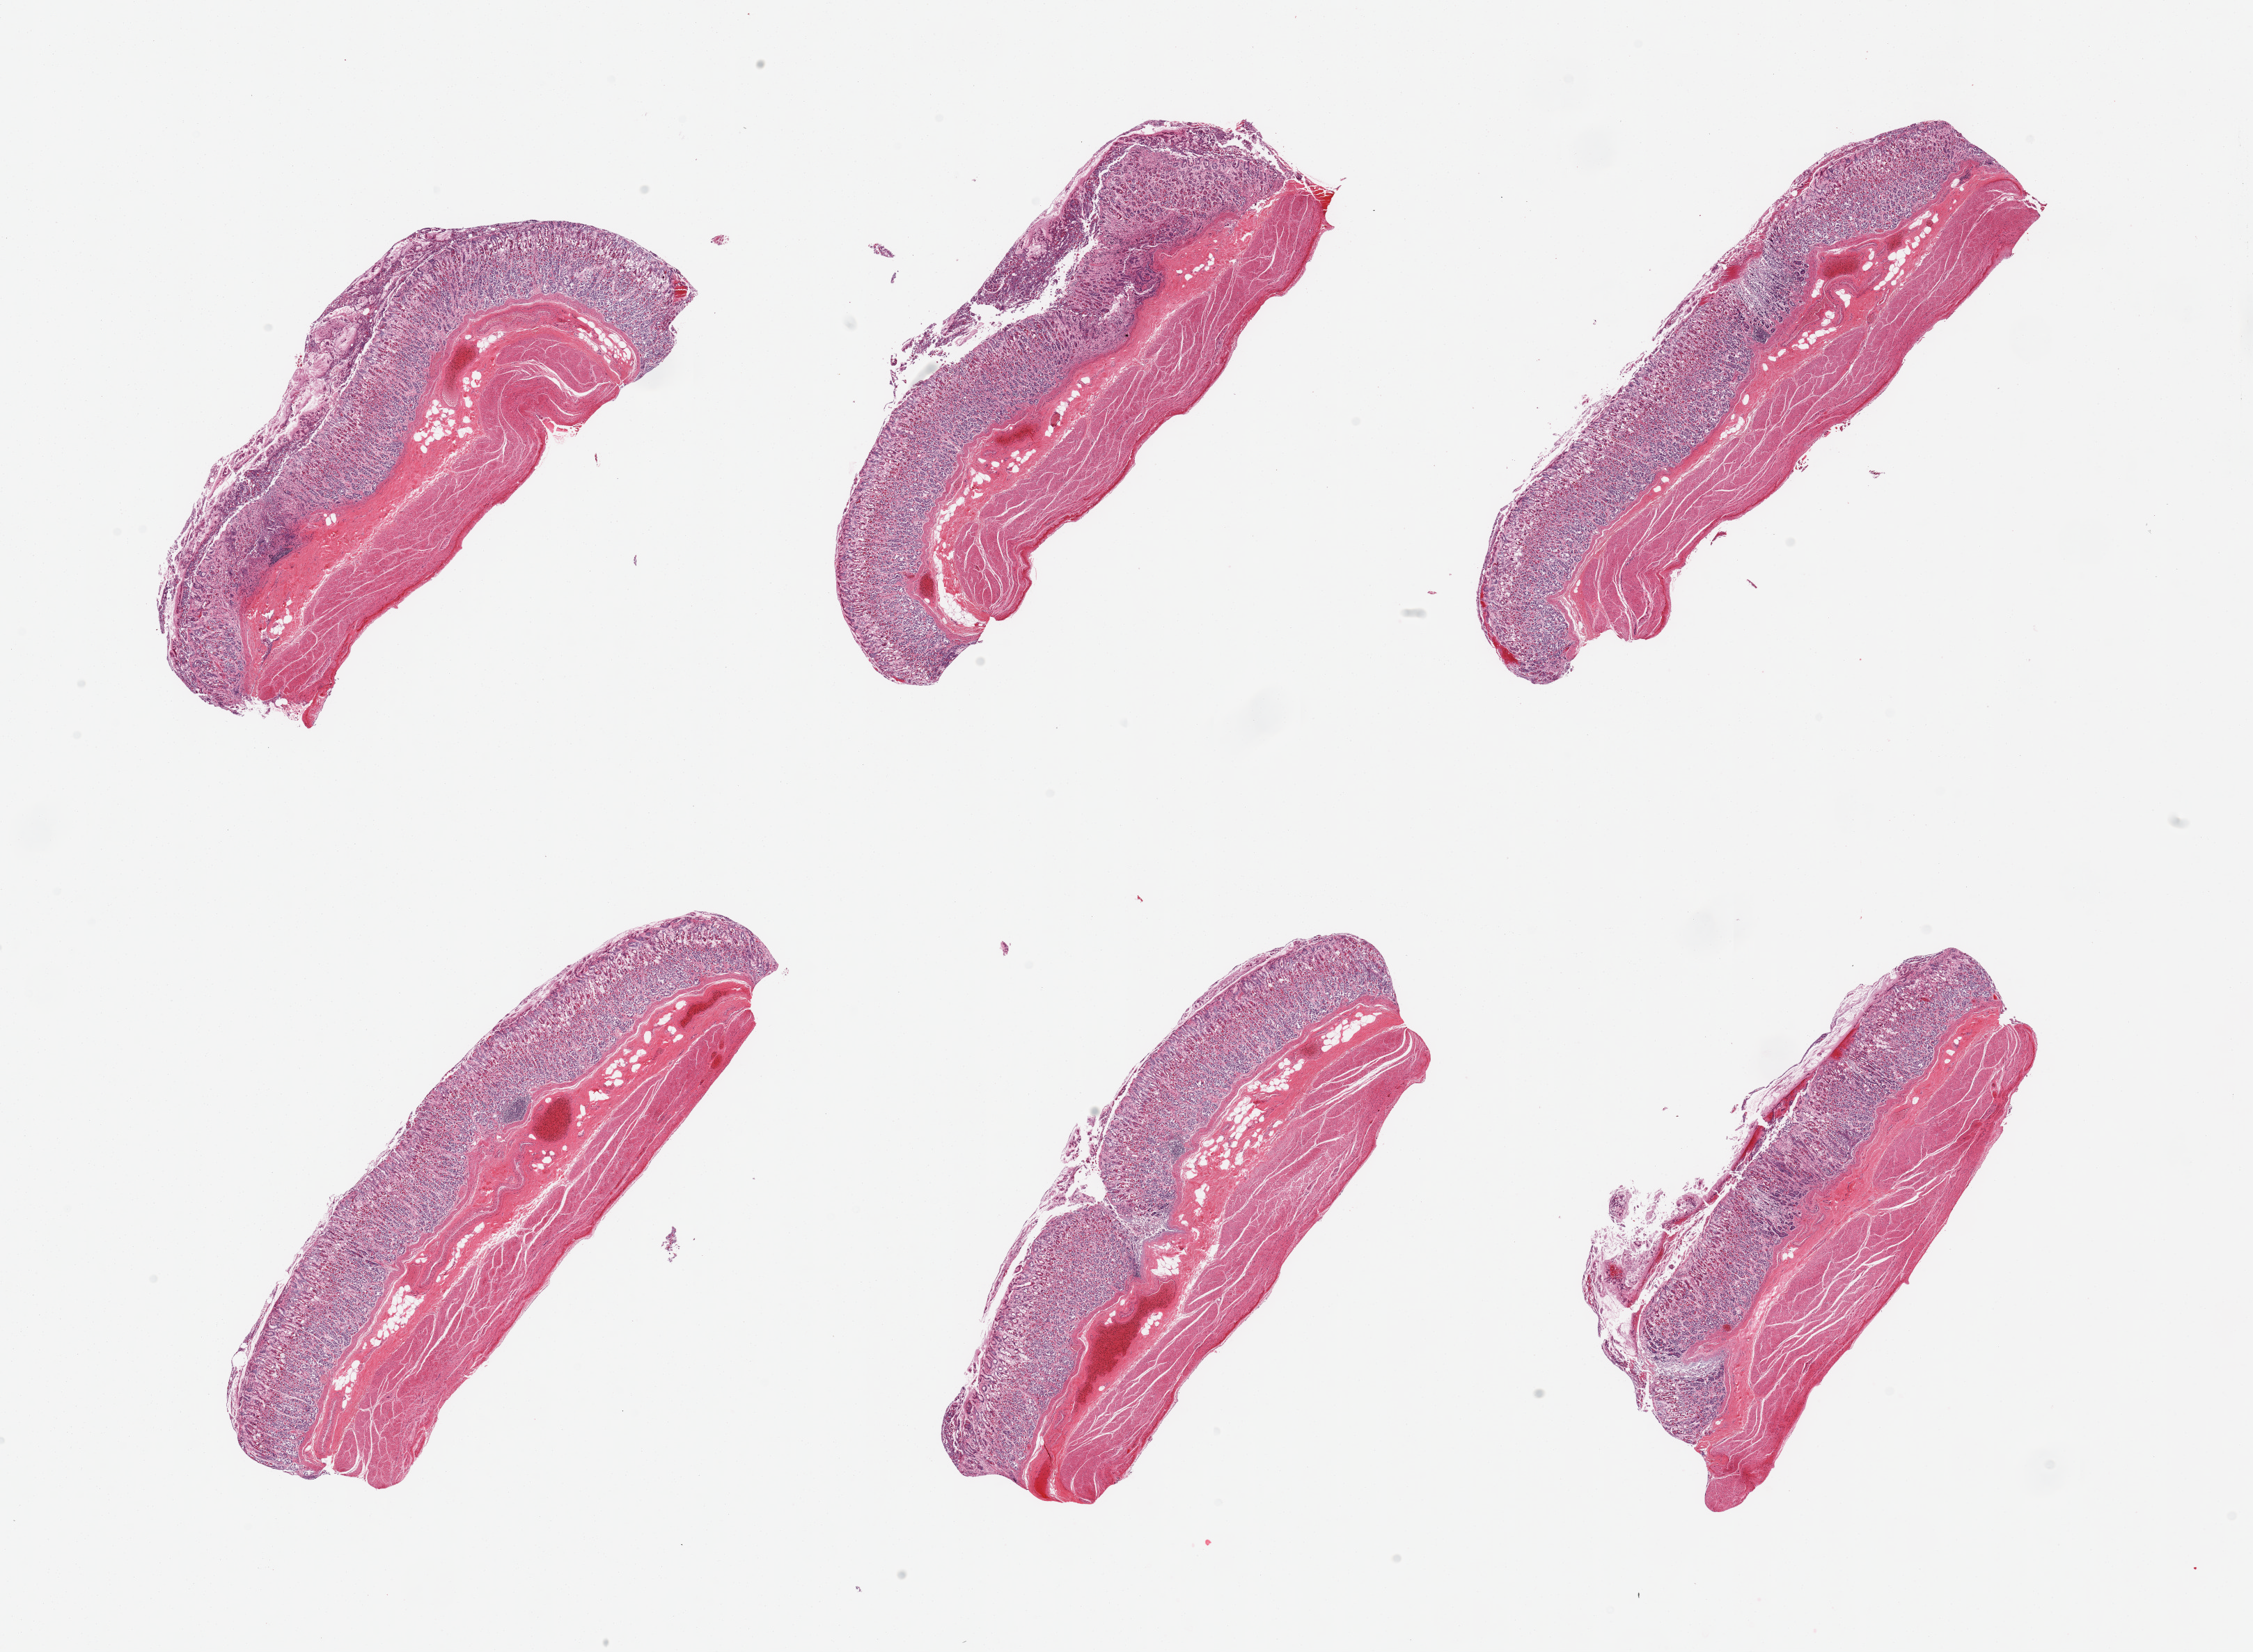
Digitized haematoxylin and eosin-stained section, brightfield — shown as a low-resolution overview of the whole scanned area (about 25.6 x 18.8 mm). PAXgene-fixed paraffin-embedded (PFPE) section. Section of stomach (target tissue). Donor tissue sample. Donor: male.
- pathologist's review note for this sample: 6 pieces; full thickness sections; congestion